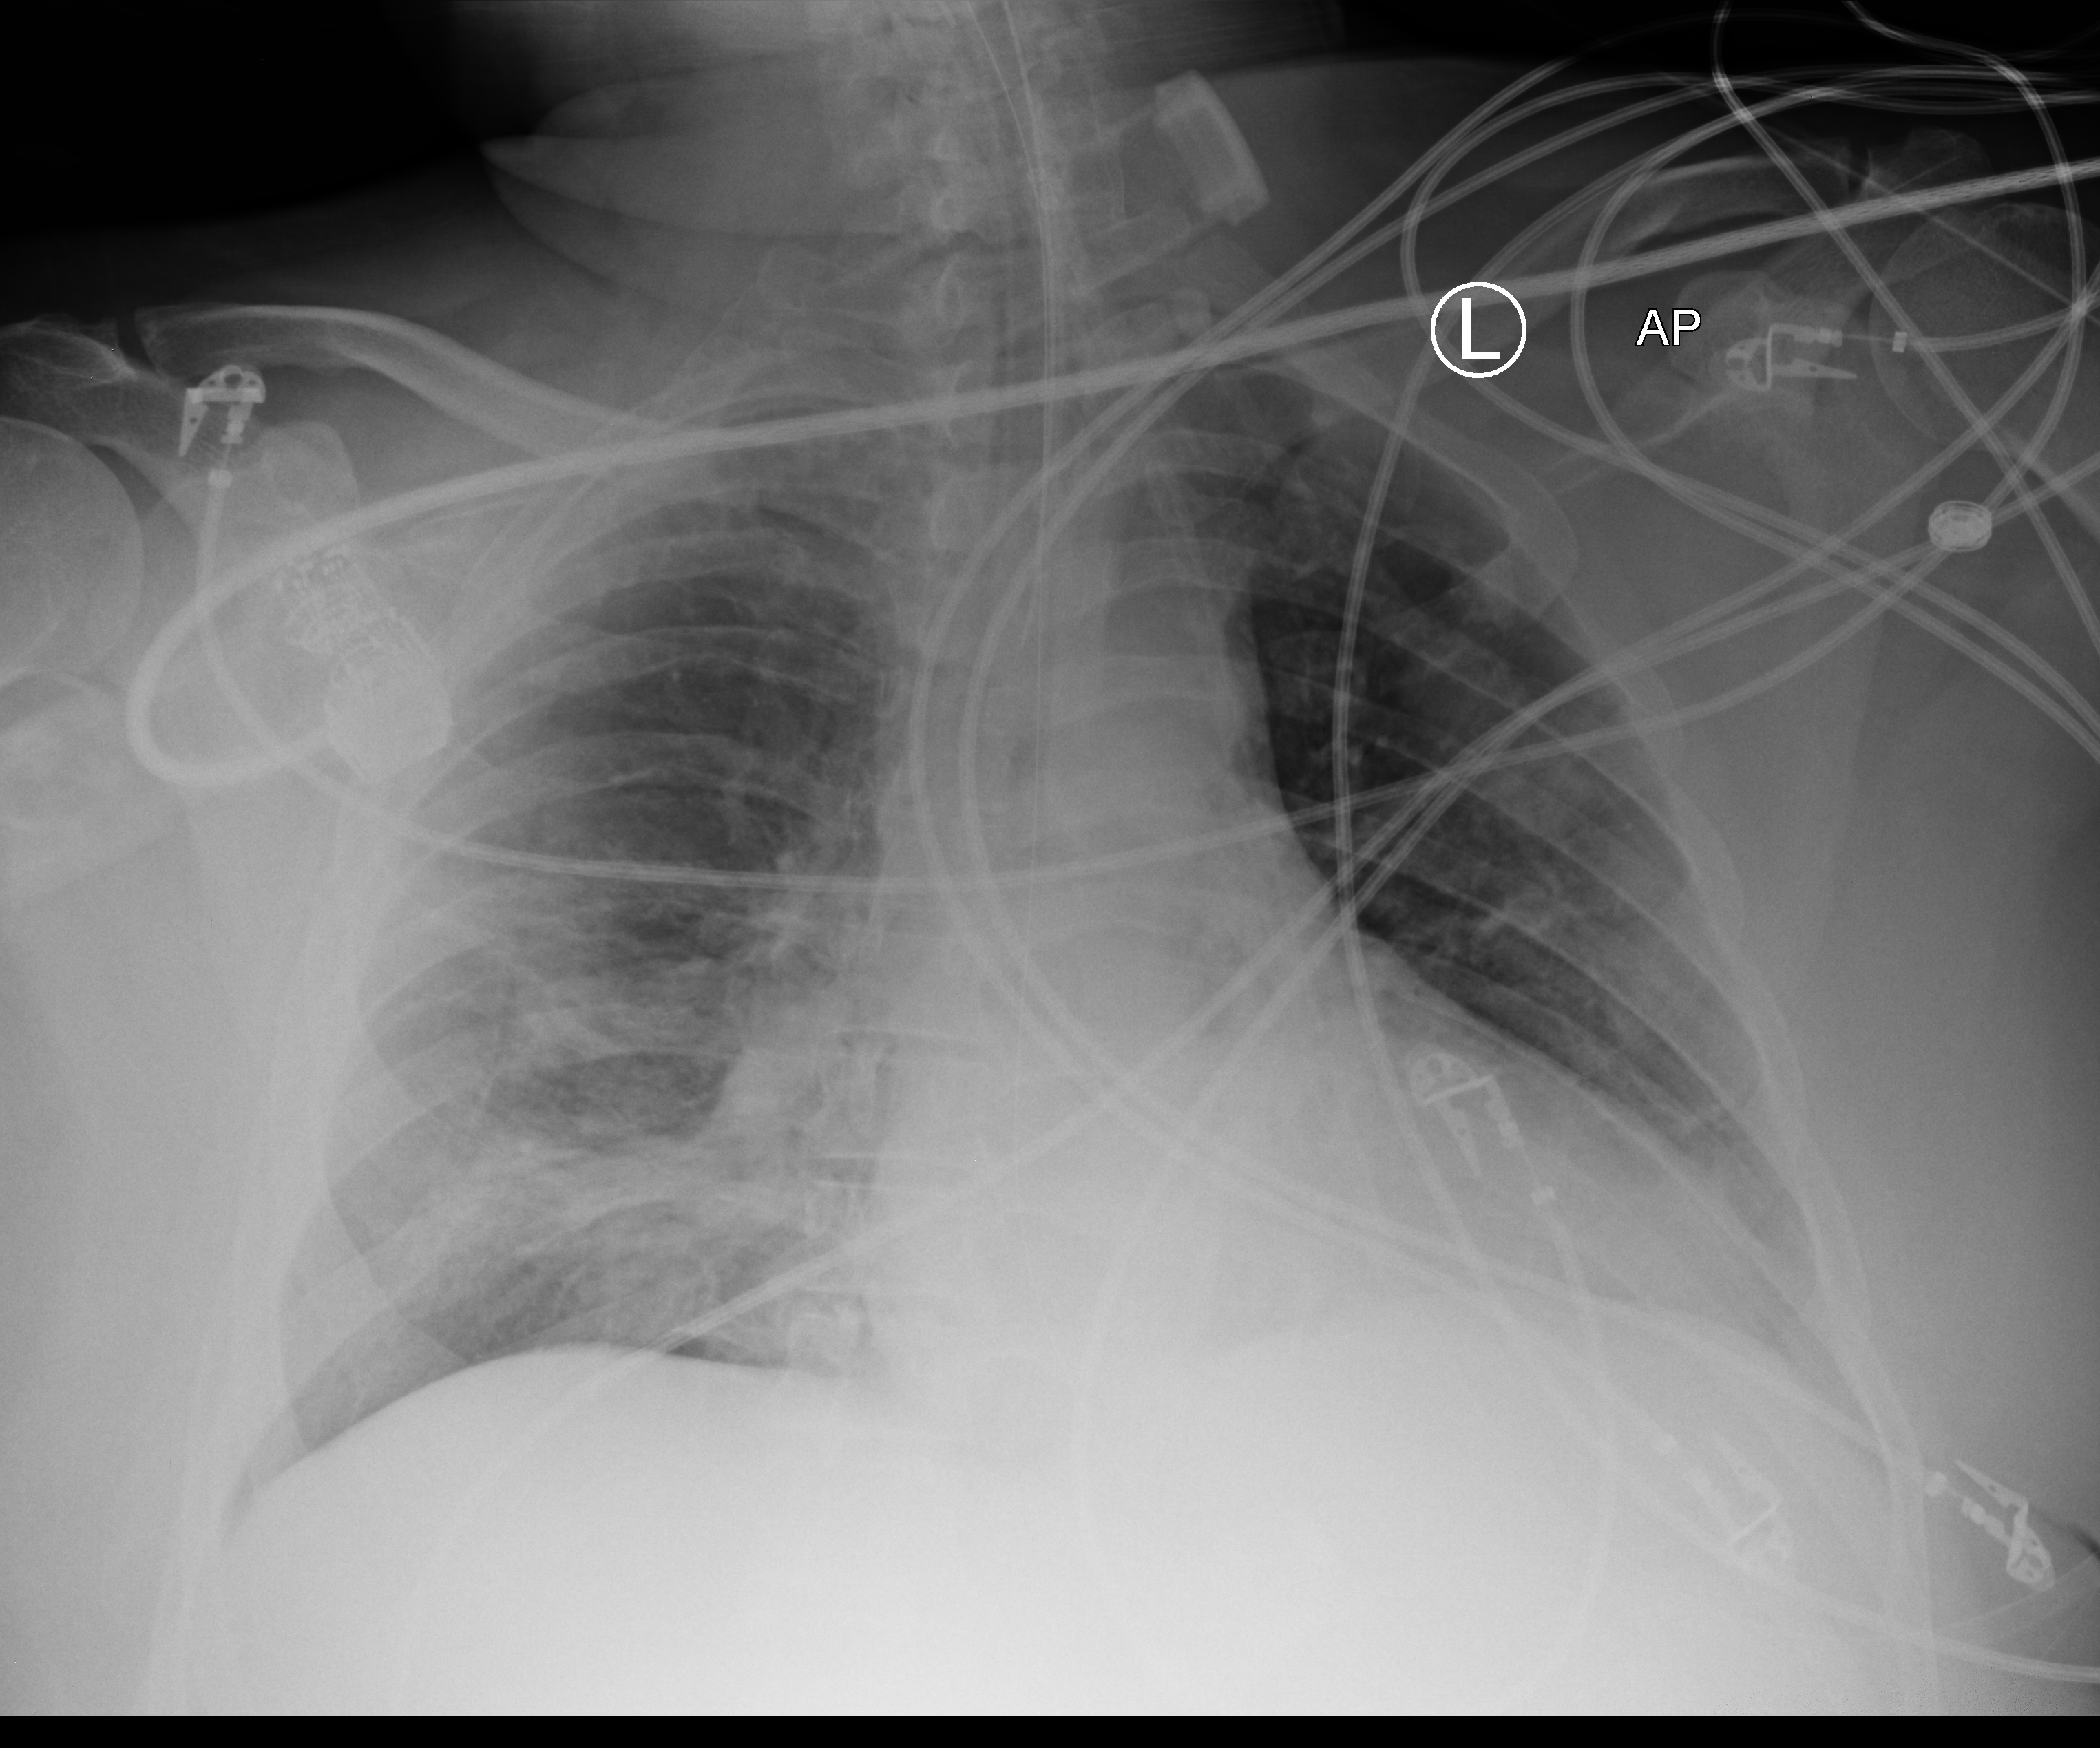
Portable chest radiograph, anteroposterior (AP) projection. Male patient hospitalised with COVID-19, age 60–74 years.
Admission-level facts for this patient (not findings on this image; timing relative to this image not recorded): smoking status (admission record): former; mechanically ventilated during this hospital stay: yes.